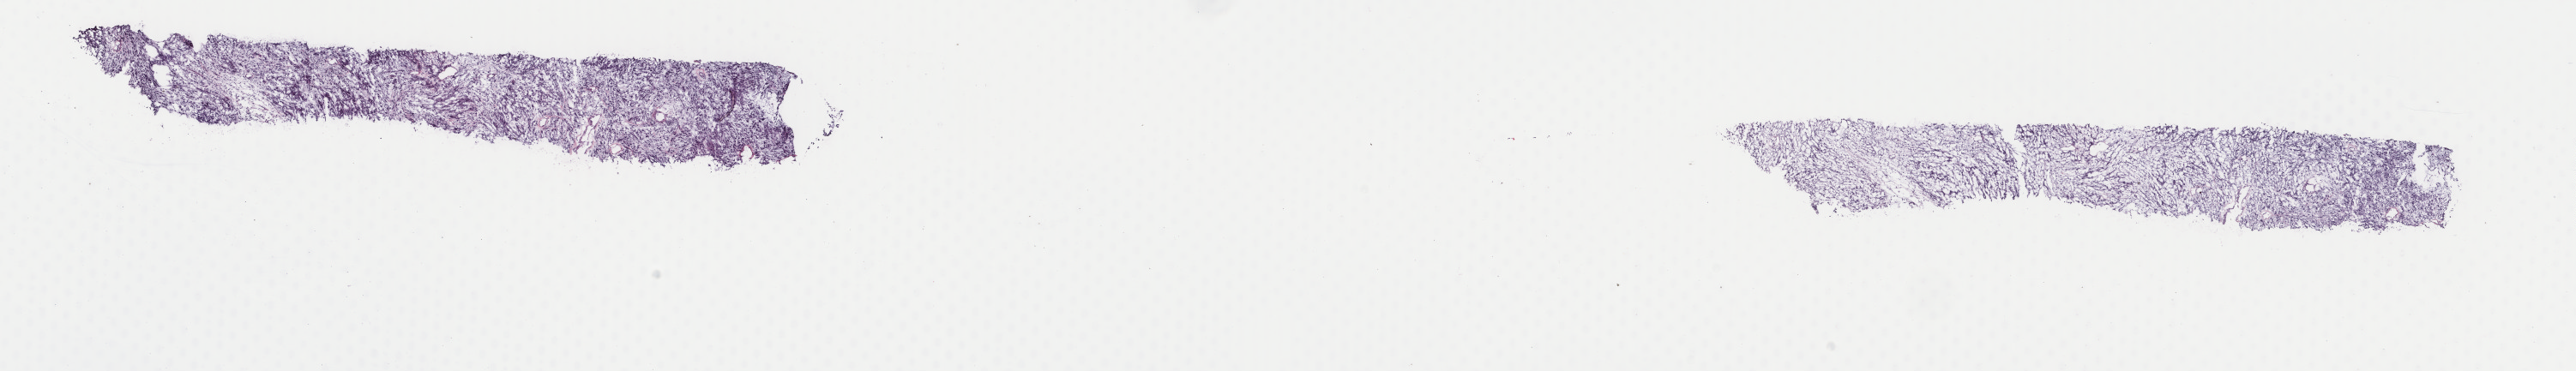
H&E-stained whole-slide image, low-resolution overview of the scanned area, about 23.8 x 3.4 mm; frozen section from the top of the tissue portion; sample: primary tumour, retroperitoneum and peritoneum. Female, age 75 years at initial diagnosis. Slide review estimates, as recorded: tumour cells 100%, tumour nuclei 85%, normal cells 0%, stromal cells 0%, necrosis 0%. Inflammatory infiltration, as recorded: lymphocyte infiltration 1%, monocyte infiltration 0%, neutrophil infiltration 0%.
• pathologic diagnosis: Leiomyosarcoma, NOS (retroperitoneum)